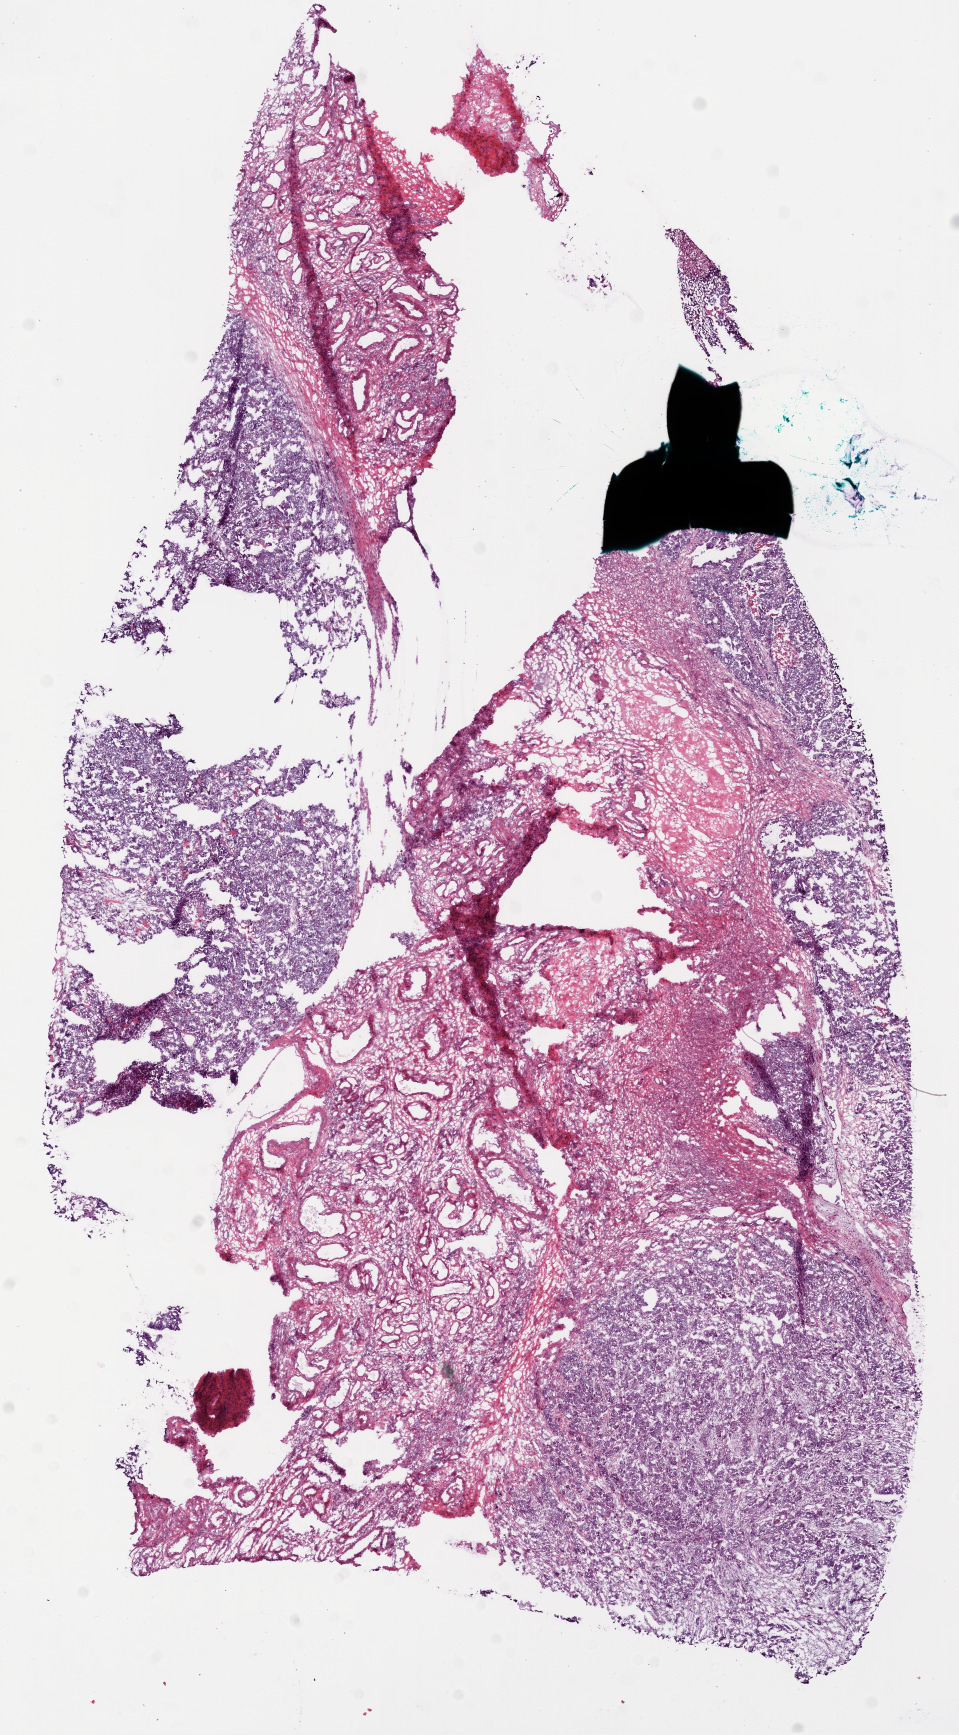
Whole-slide histology image, H&E-stained, a low-resolution overview of the entire scanned area, about 7.7 x 14.0 mm (slide scanned at 20x), frozen section, ovary, primary tumour sample. Patient: female, age at initial diagnosis 70 years. Histologic grade: G3 (poorly differentiated). Pathologist review of this section (percent, as recorded): tumour cells 40%, tumour nuclei 89%, normal cells 0%, stromal cells 52%, necrosis 8%.
Diagnosis: Serous cystadenocarcinoma, NOS. FIGO stage: IIIC. Laterality: bilateral.